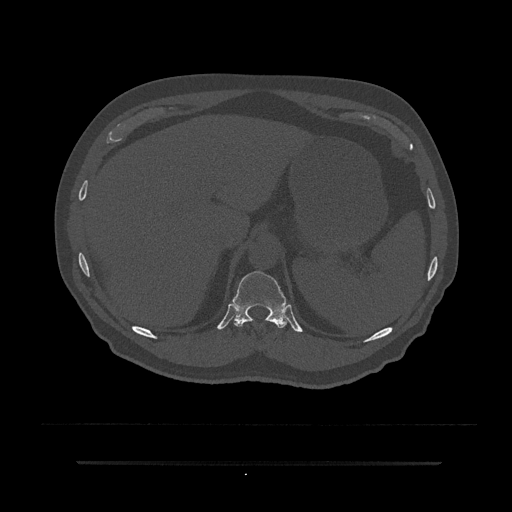
CT including the spine, one axial slice; slice 285 of 797 in the series (ordered by position); reconstruction kernel Br40s/3; 120 kVp; bone window (W 1800 / L 400 HU); 0.5 mm slice thickness; 512 × 512 image matrix, field of view 464 × 464 mm. Patient: male, 59 years. From the clinical record (not read from this slice): primary cancer: bile ducts; vertebrae with lytic lesions (as recorded): T10.
Structures marked on this image (semi-automatically segmented with operator editing):
- T11 vertebra: bounding box (x1, y1, x2, y2) in pixels: (231, 271, 290, 328)